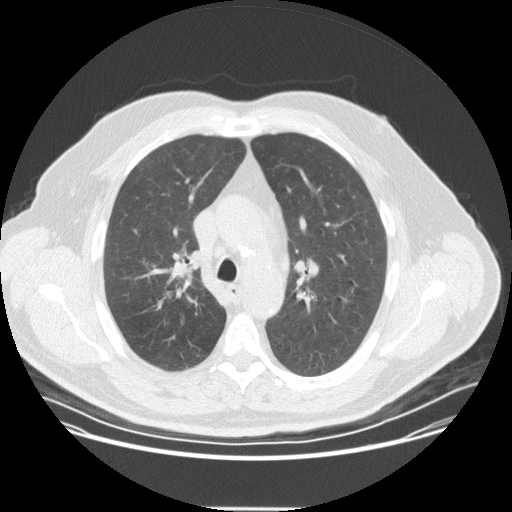
Chest CT (low-dose screening protocol), one axial image; second screening round (one year after baseline); lung window (W 1500 / L -600 HU); 2.5 mm slice thickness; slice 114 of 351 in the series; 512 × 512 image matrix. Male, age 57 years at enrolment. Current smoker at enrolment.
Lesion marked by an expert reader, bounding box <144,248,211,314> (left, top, right, bottom; pixels). The exam's reader record, not a measurement of the box and not confirmed to be the same lesion: non-calcified nodule or mass ≥4 mm, right upper lobe, 20 × 16 mm, spiculated (stellate) margins, soft tissue attenuation, pre-existing on the prior screen: no. Participant outcome: lung cancer diagnosed 35 days after this screen — non-small cell carcinoma, right upper lobe, poorly differentiated (G3), stage IIA (AJCC 6th edition), 25 mm at pathology.